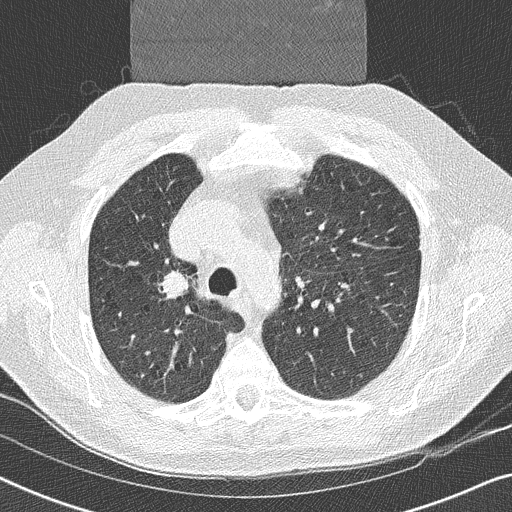
Low-dose screening chest CT, one axial slice; 120 kVp; lung window (W 1500 / L -600 HU); 2 mm slice thickness; 512 × 512 image matrix.
Structures marked on this image (expert manual segmentation):
- lesion 1 (tumor, upper lobe of right lung): box from (x=164, y=272) to (x=190, y=297) px